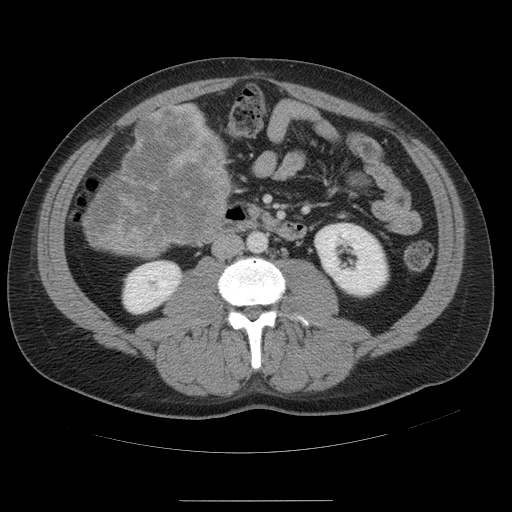
Contrast-enhanced abdominal CT, one axial slice; position 12 of 54 along the scan axis; intravenous contrast given; soft-tissue window (W 400 / L 40 HU); 5 mm slice thickness; 512 × 512 image matrix. Male patient, age 40 years. Case-level facts recorded for this patient, not image findings: diagnosis: colorectal cancer liver metastases, imaged before liver resection; multiple liver metastases: no; largest metastasis: 15 cm.
Annotated regions visible in this slice (outlined manually by an expert reader):
- liver: bounding box <84,103,232,258> (left, top, right, bottom; pixels)
- liver metastasis: <83,108,228,259>